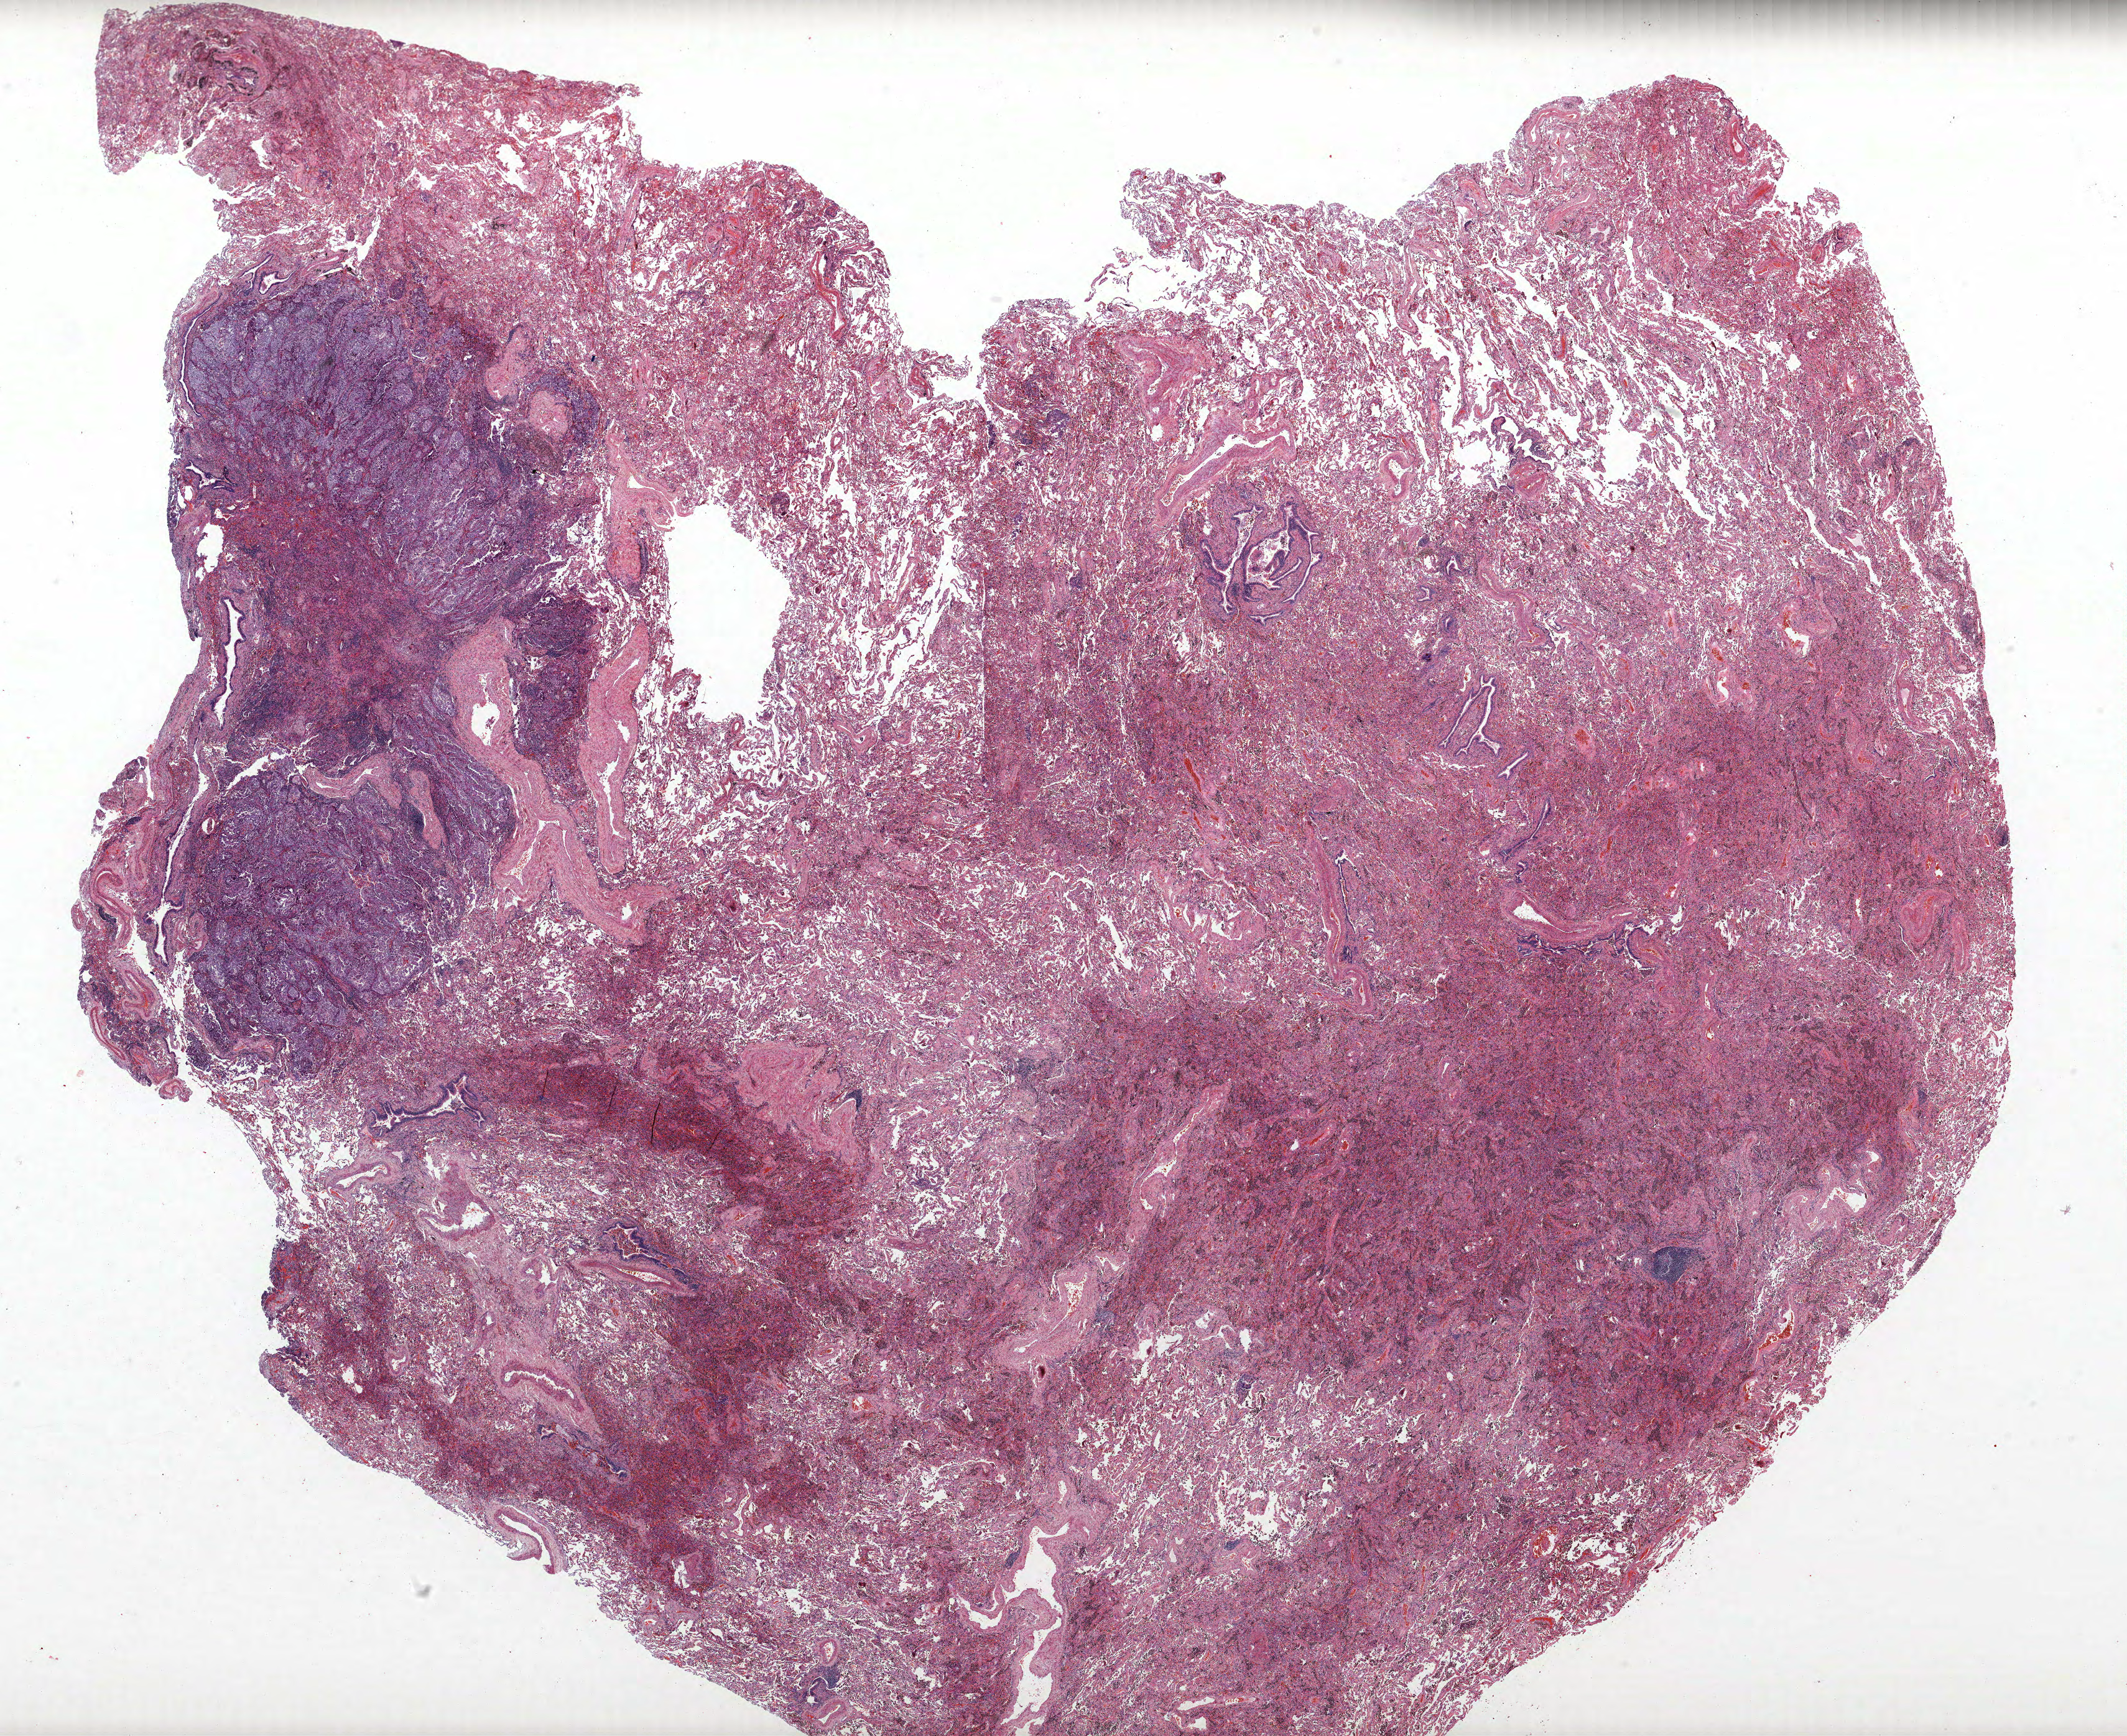
H&E-stained whole-slide image, shown as a low-resolution overview of the whole scanned area (about 27.4 x 22.3 mm, from a 40x scan); FFPE section; lung. Female patient, aged 58 at enrolment. Current smoker at enrolment. Grade: moderately differentiated (G2).
ICD-O-3 topography: lower lobe of lung (C34.3). Participant's lung-cancer diagnosis: Adenocarcinoma, NOS. Primary tumour location (clinical record): left lower lobe. Tumour size (pathology): 14 mm. Stage (AJCC 6th edition): IIIB.